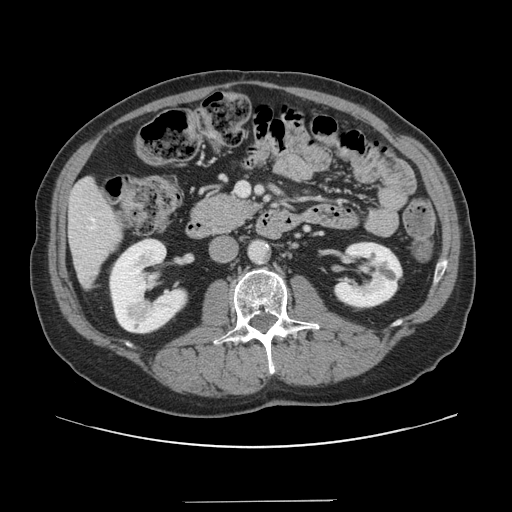
Contrast-enhanced abdominal CT, one axial slice; slice 50 of 151 in the series (ordered by position); intravenous contrast given; soft-tissue window (W 400 / L 40 HU); 2.5 mm slice thickness; 512 × 512 image matrix, field of view 399 × 399 mm. Male patient, age 63 years. From the clinical record (not read from this slice): diagnosis: colorectal cancer liver metastases, imaged before liver resection; multiple liver metastases: no; largest metastasis: 2.1 cm; disease in both lobes: no.
Outlined on this slice (expert manual segmentation):
- hepatic veins: bounding box [x1, y1, x2, y2] px = [91, 219, 94, 228]
- liver: [70, 179, 122, 285]
- planned liver remnant (the part of the liver to remain after resection): [69, 179, 122, 285]
- portal vein (with intrahepatic branches): [237, 183, 249, 196]